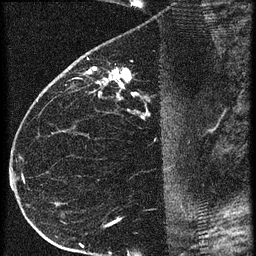
Breast MRI (dynamic contrast-enhanced), one sagittal slice. 3 images stored at this slice position (order not interpretable as contrast timing). 1.5 T. TE 4.2 ms, TR 20.4 ms. 1.5 mm slice thickness. 256 × 256 image matrix, field of view 180 × 180 mm. Female patient, age 35 years. Case-level facts recorded for this patient, not image findings: setting: breast cancer imaged before/during neoadjuvant chemotherapy; receptor status: HR-positive, HER2-negative.
Outlined on this slice (semi-automatically segmented with operator editing):
- analysis volume of interest (the breast-tissue region the enhancement analysis was run in; not a lesion): bounding box <65,60,169,119> (left, top, right, bottom; pixels)
- tumour enhancement mask (voxels above the 90 % enhancement threshold inside the analysis volume of interest): <88,68,147,117>